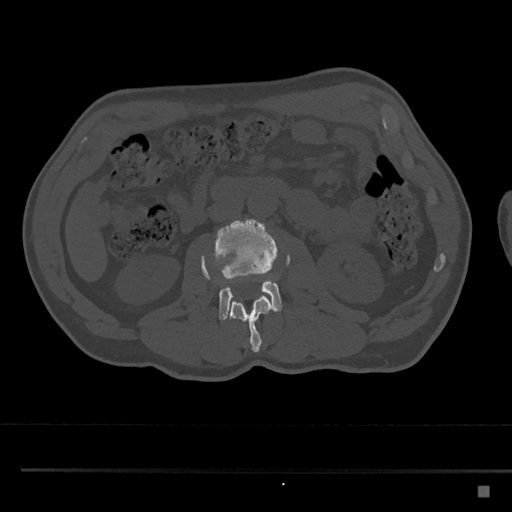
CT including the spine, one axial slice. Slice 727 of 797 in the series (ordered by position). Reconstruction kernel Br40s/3. Bone window (W 1800 / L 400 HU). 512 × 512 image matrix, field of view 391 × 391 mm. Male patient, age 59 years. Case-level facts recorded for this patient, not image findings: primary cancer: prostate.
Outlined on this slice (semi-automatically segmented with operator editing):
- L2 vertebra: box from (x=202, y=256) to (x=273, y=352) px
- L3 vertebra: (x=201, y=219)–(x=291, y=320)